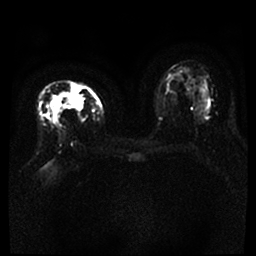
Breast MRI, one axial slice. Position 21 of 46 along the scan axis. Diffusion-weighted series; image 2 of 4 stored at this slice position (different b-values; order by instance number). 1.5 T. 4 mm slice thickness. 256 × 256 image matrix, field of view 360 × 360 mm. Female patient.
Annotated regions visible in this slice (outlined manually by an expert reader):
- tumour on diffusion-weighted imaging: bounding box <52,85,83,112> (left, top, right, bottom; pixels)